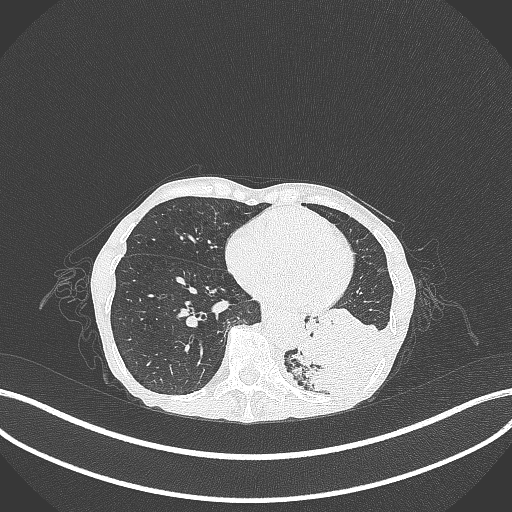
Chest CT, one axial slice. Position 83 of 347 along the scan axis. Reconstruction kernel B70f. 120 kVp. Lung window (W 1500 / L -600 HU). 1 mm slice thickness. 512 × 512 image matrix, field of view 400 × 400 mm. Female patient, age 70 years. Case-level facts recorded for this patient, not image findings: clinical TNM (as recorded): T3 N0 M0; histopathological grade: G3.
Annotated regions visible in this slice (rectangle marked by the reading radiologist):
- lung tumour (recorded histology: small cell carcinoma): box from (x=287, y=313) to (x=384, y=398) px